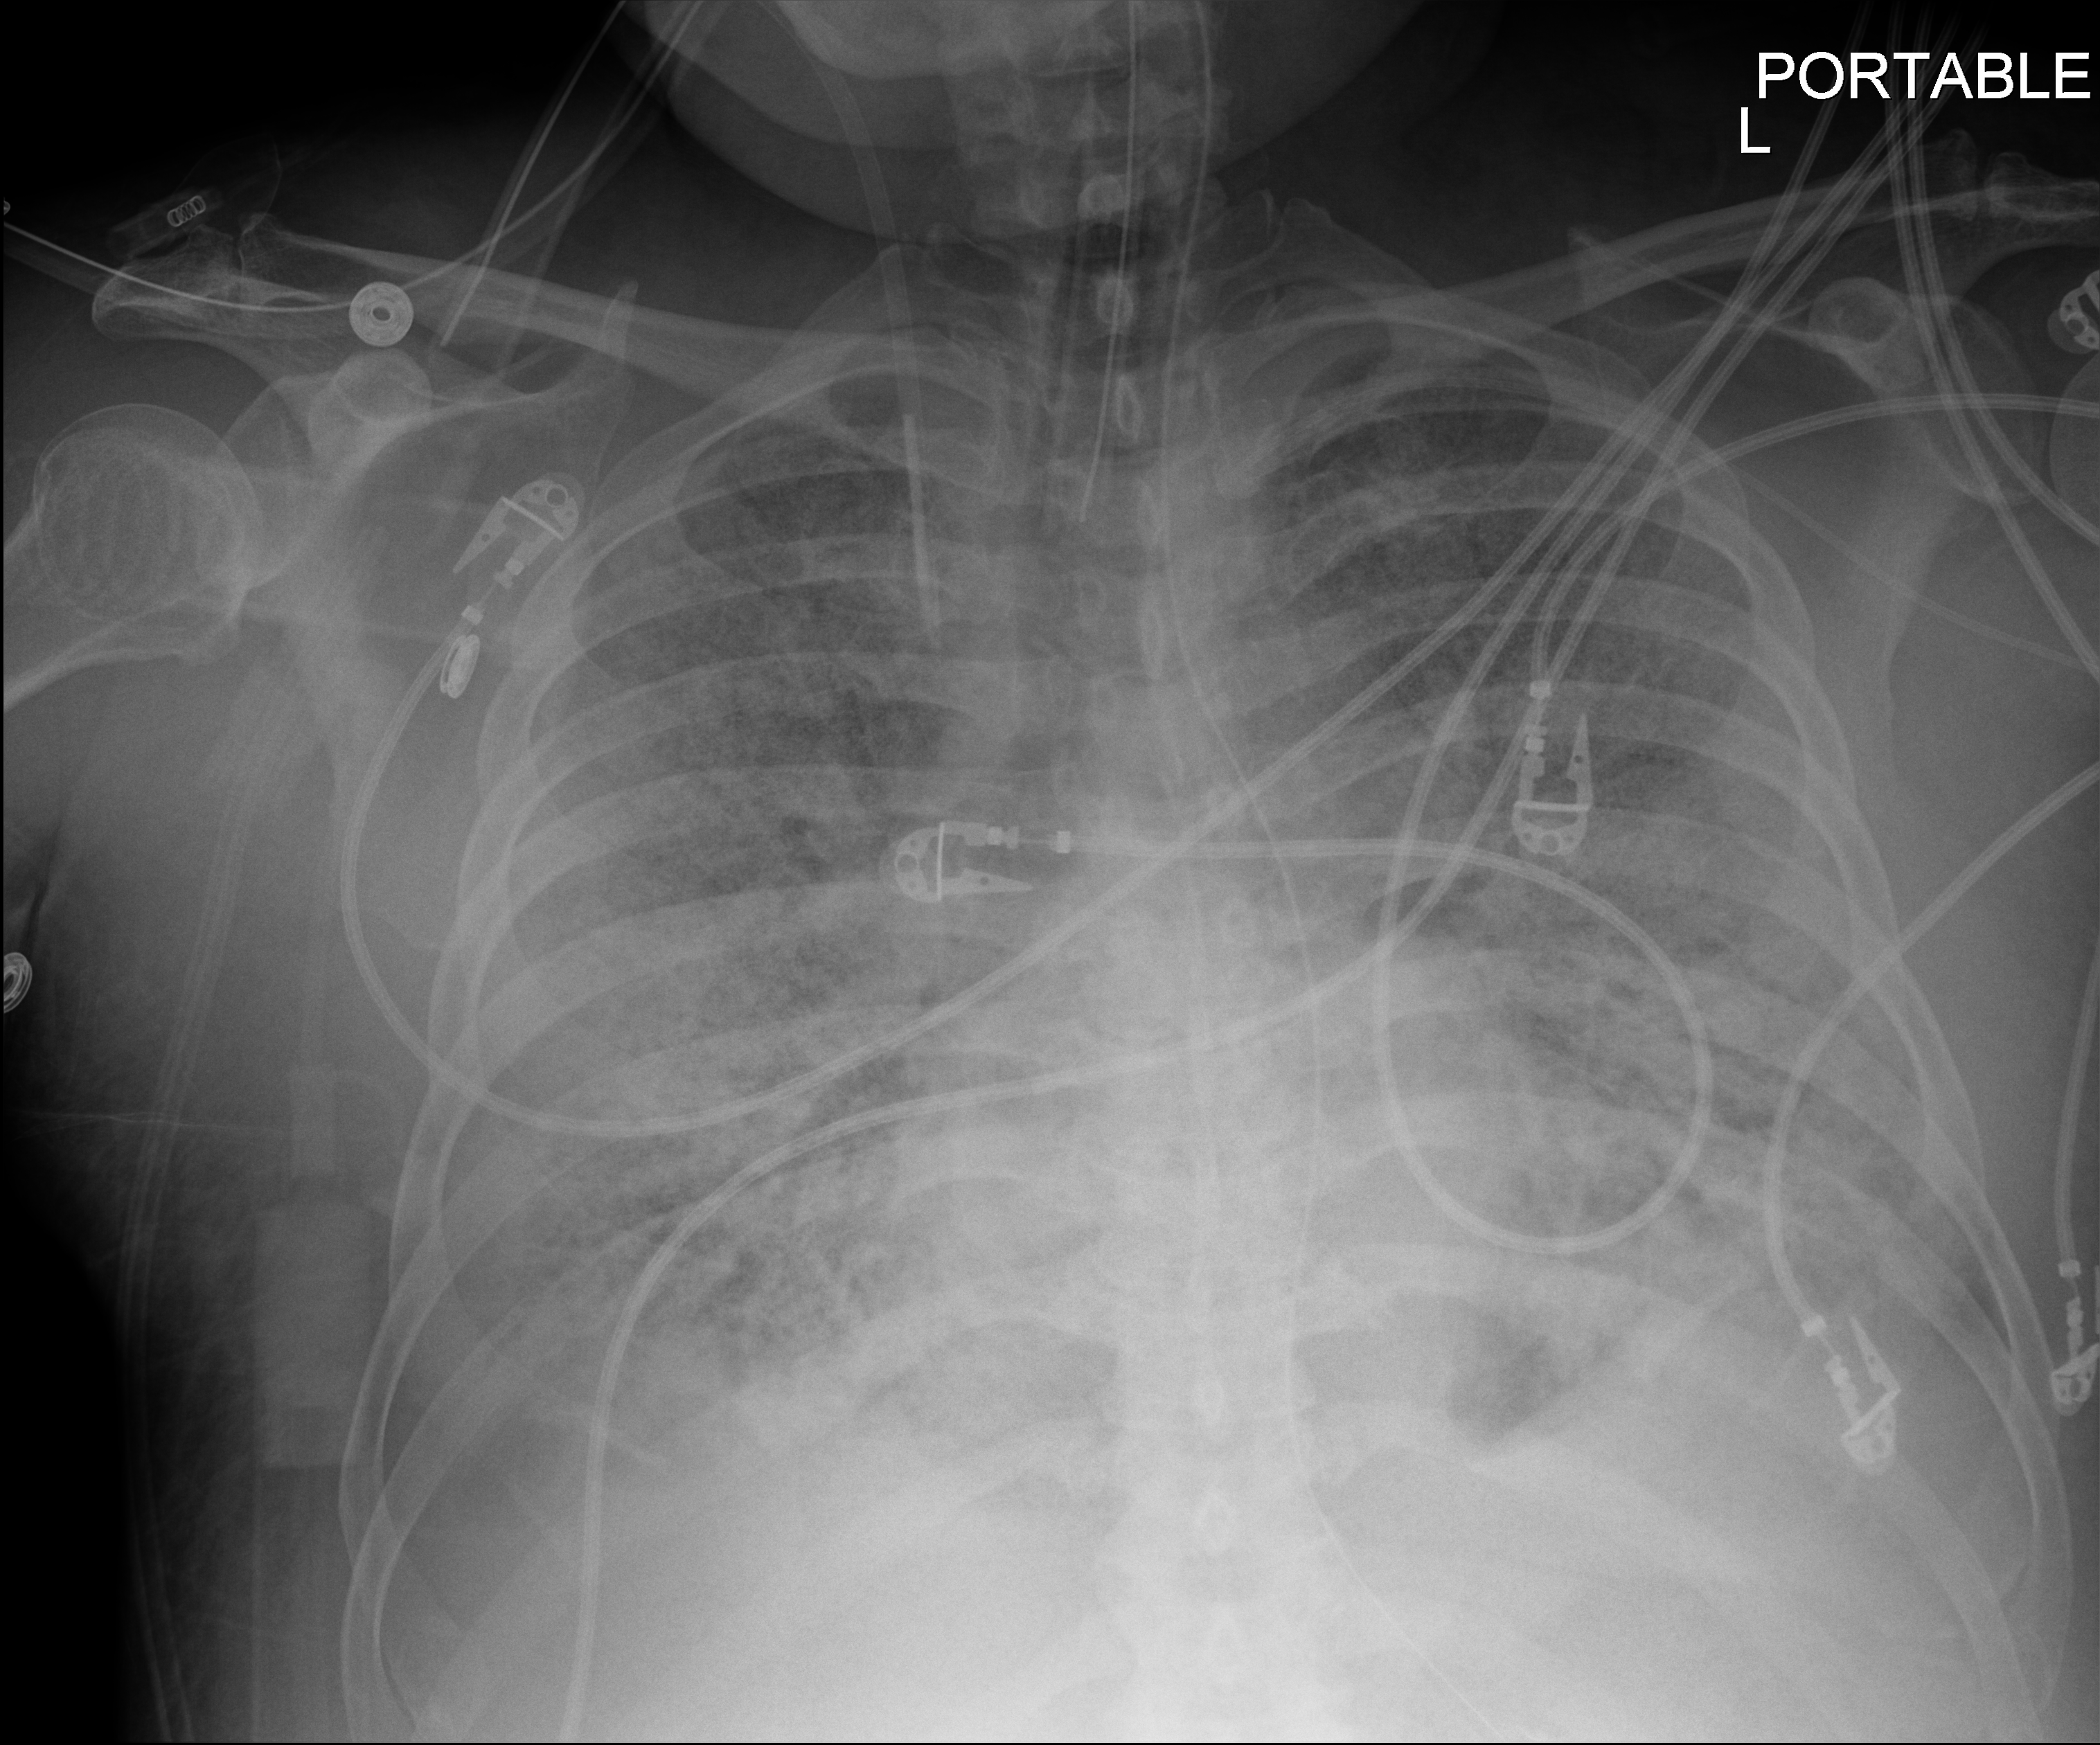
Bedside chest radiograph (digital radiography). Male patient hospitalised with COVID-19, age 60–74 years.
Admission-level facts for this patient (not findings on this image; timing relative to this image not recorded):
- mechanically ventilated during this hospital stay: yes